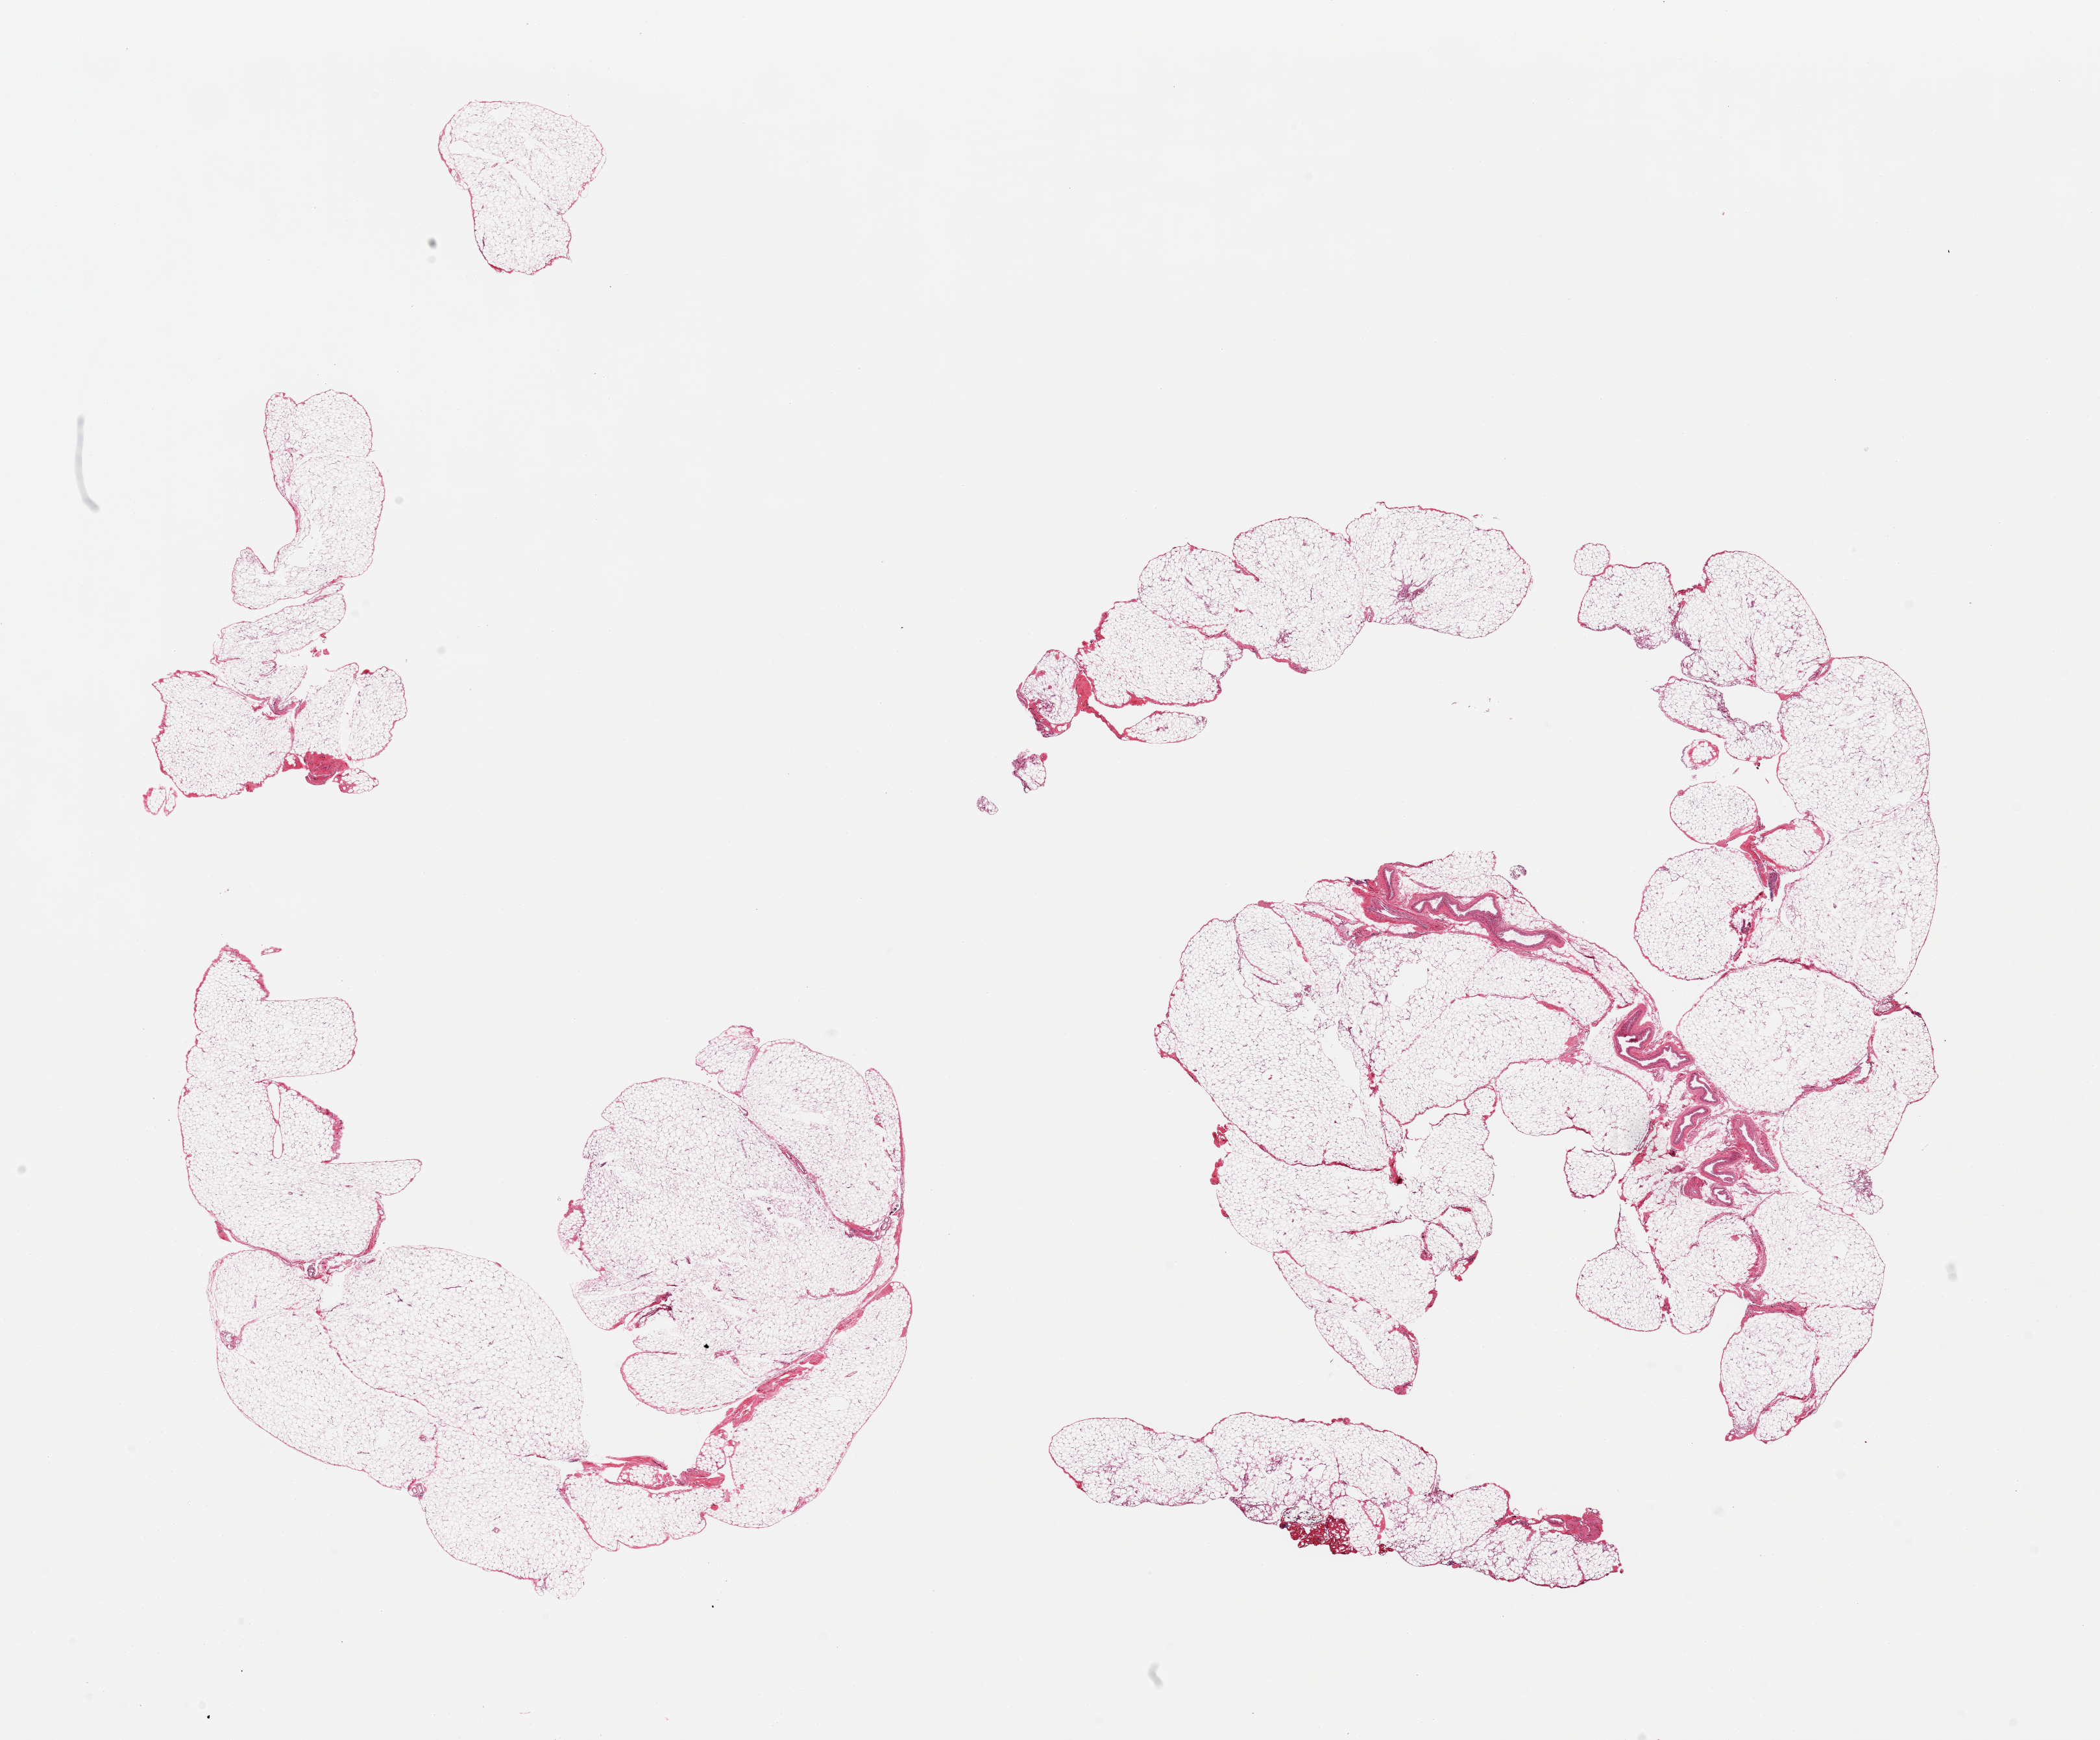
Whole-slide image, hematoxylin and eosin (H&E) stain, brightfield, shown as a low-resolution overview of the whole scanned area (about 25.6 x 21.2 mm, slide scanned at 20x), PAXgene-fixed, paraffin-embedded tissue, target tissue: omentum, donor tissue sample. Donor: female.
- pathologist's review note for this sample: several fragmented pieces